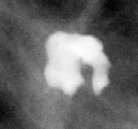
Region of interest cut from a scanned film mammogram (one marked finding); left breast; MLO view; BI-RADS breast density category 3 (scale 1–4).
- Calcifications, morphology round and regular / lucent center / dystrophic, distribution diffusely scattered; BI-RADS assessment category 2; subtlety rating 4 on a 1 (subtle) to 5 (obvious) scale; benign without callback (not worked up further).